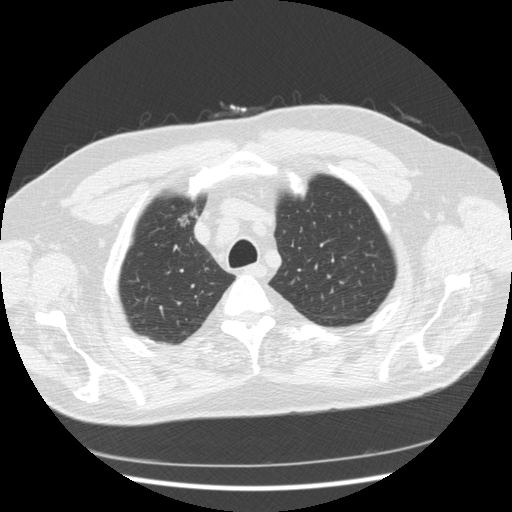
Low-dose screening chest CT, axial slice. Second screening round (one year after baseline). Lung window (W 1500 / L -600 HU). 120 kVp. 512 × 512 image matrix. Male, age 66 years at enrolment.
Expert-annotated lung lesion, bounding box <157,201,208,241> (left, top, right, bottom; pixels). No non-calcified nodule or mass ≥4 mm was recorded by the screening reader at this exam. Official screen result: positive, other. Participant outcome: lung cancer diagnosed 603 days after this screen (after the third annual screen) — bronchiolo-alveolar adenocarcinoma, NOS, right upper lobe, moderately differentiated (G2), stage IA (AJCC 6th edition), 12 mm at pathology.